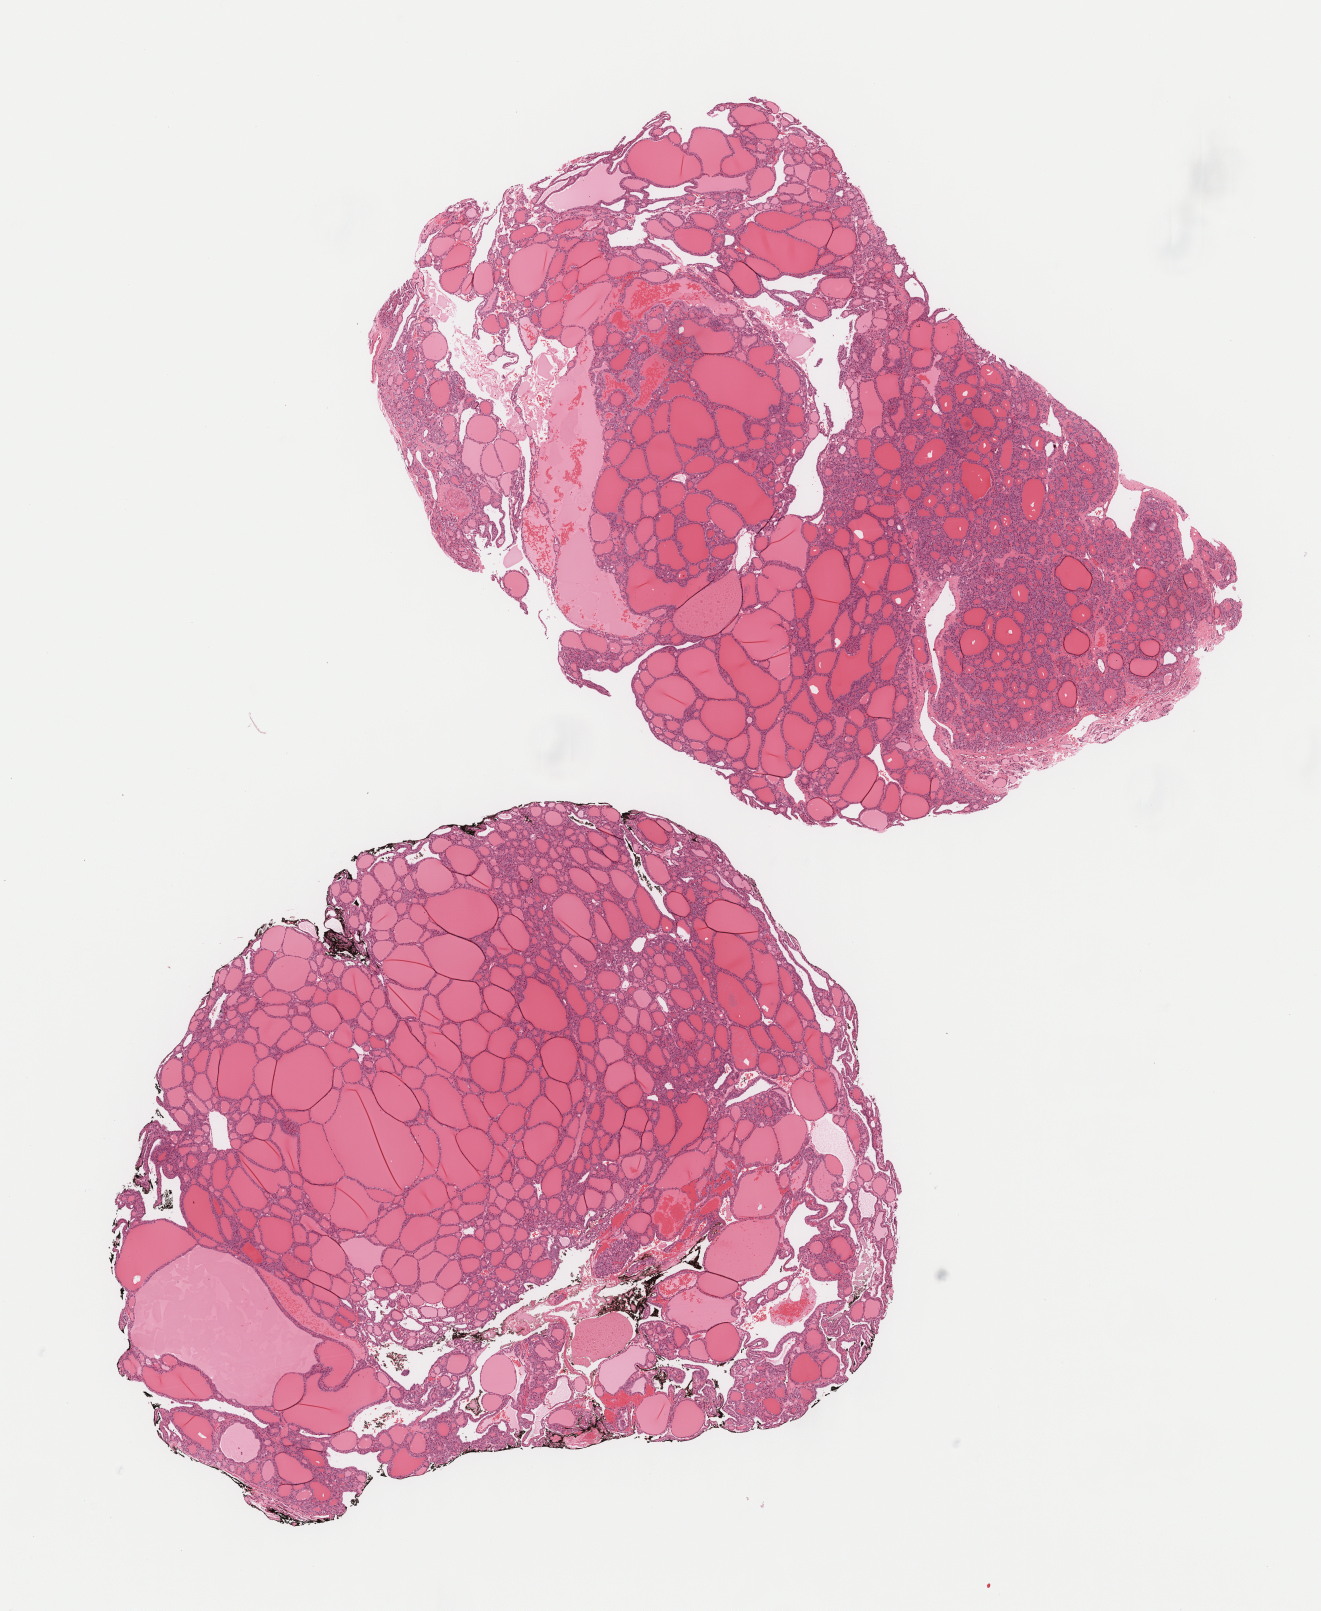
H&E-stained whole-slide image, low-resolution overview of the scanned area, about 10.6 x 13.0 mm (acquisition: 40x scan); FFPE section; sample: primary tumour, thyroid. Patient: female, age at initial diagnosis 33 years.
Pathologic diagnosis: Papillary carcinoma, follicular variant (thyroid gland). Lymph nodes positive (case pathology): 0 of 1 examined. AJCC pathologic stage: I (7th edition). Laterality: right.